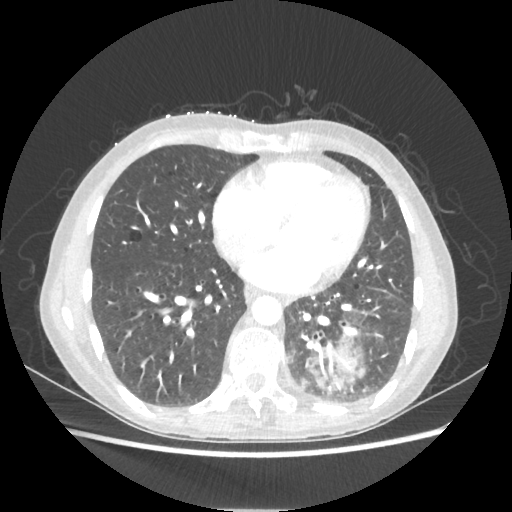
Chest CT, one axial slice. Position 82 of 221 along the scan axis. Reconstruction kernel STANDARD. Lung window (W 1500 / L -600 HU). 512 × 512 image matrix, field of view 360 × 360 mm. Patient: female, 53 years. From the clinical record (not read from this slice): clinical TNM (as recorded): T3 N0 M0.
Annotated regions visible in this slice (bounding box drawn by a radiologist):
- lung tumour (recorded histology: adenocarcinoma): box from (x=309, y=344) to (x=358, y=389) px